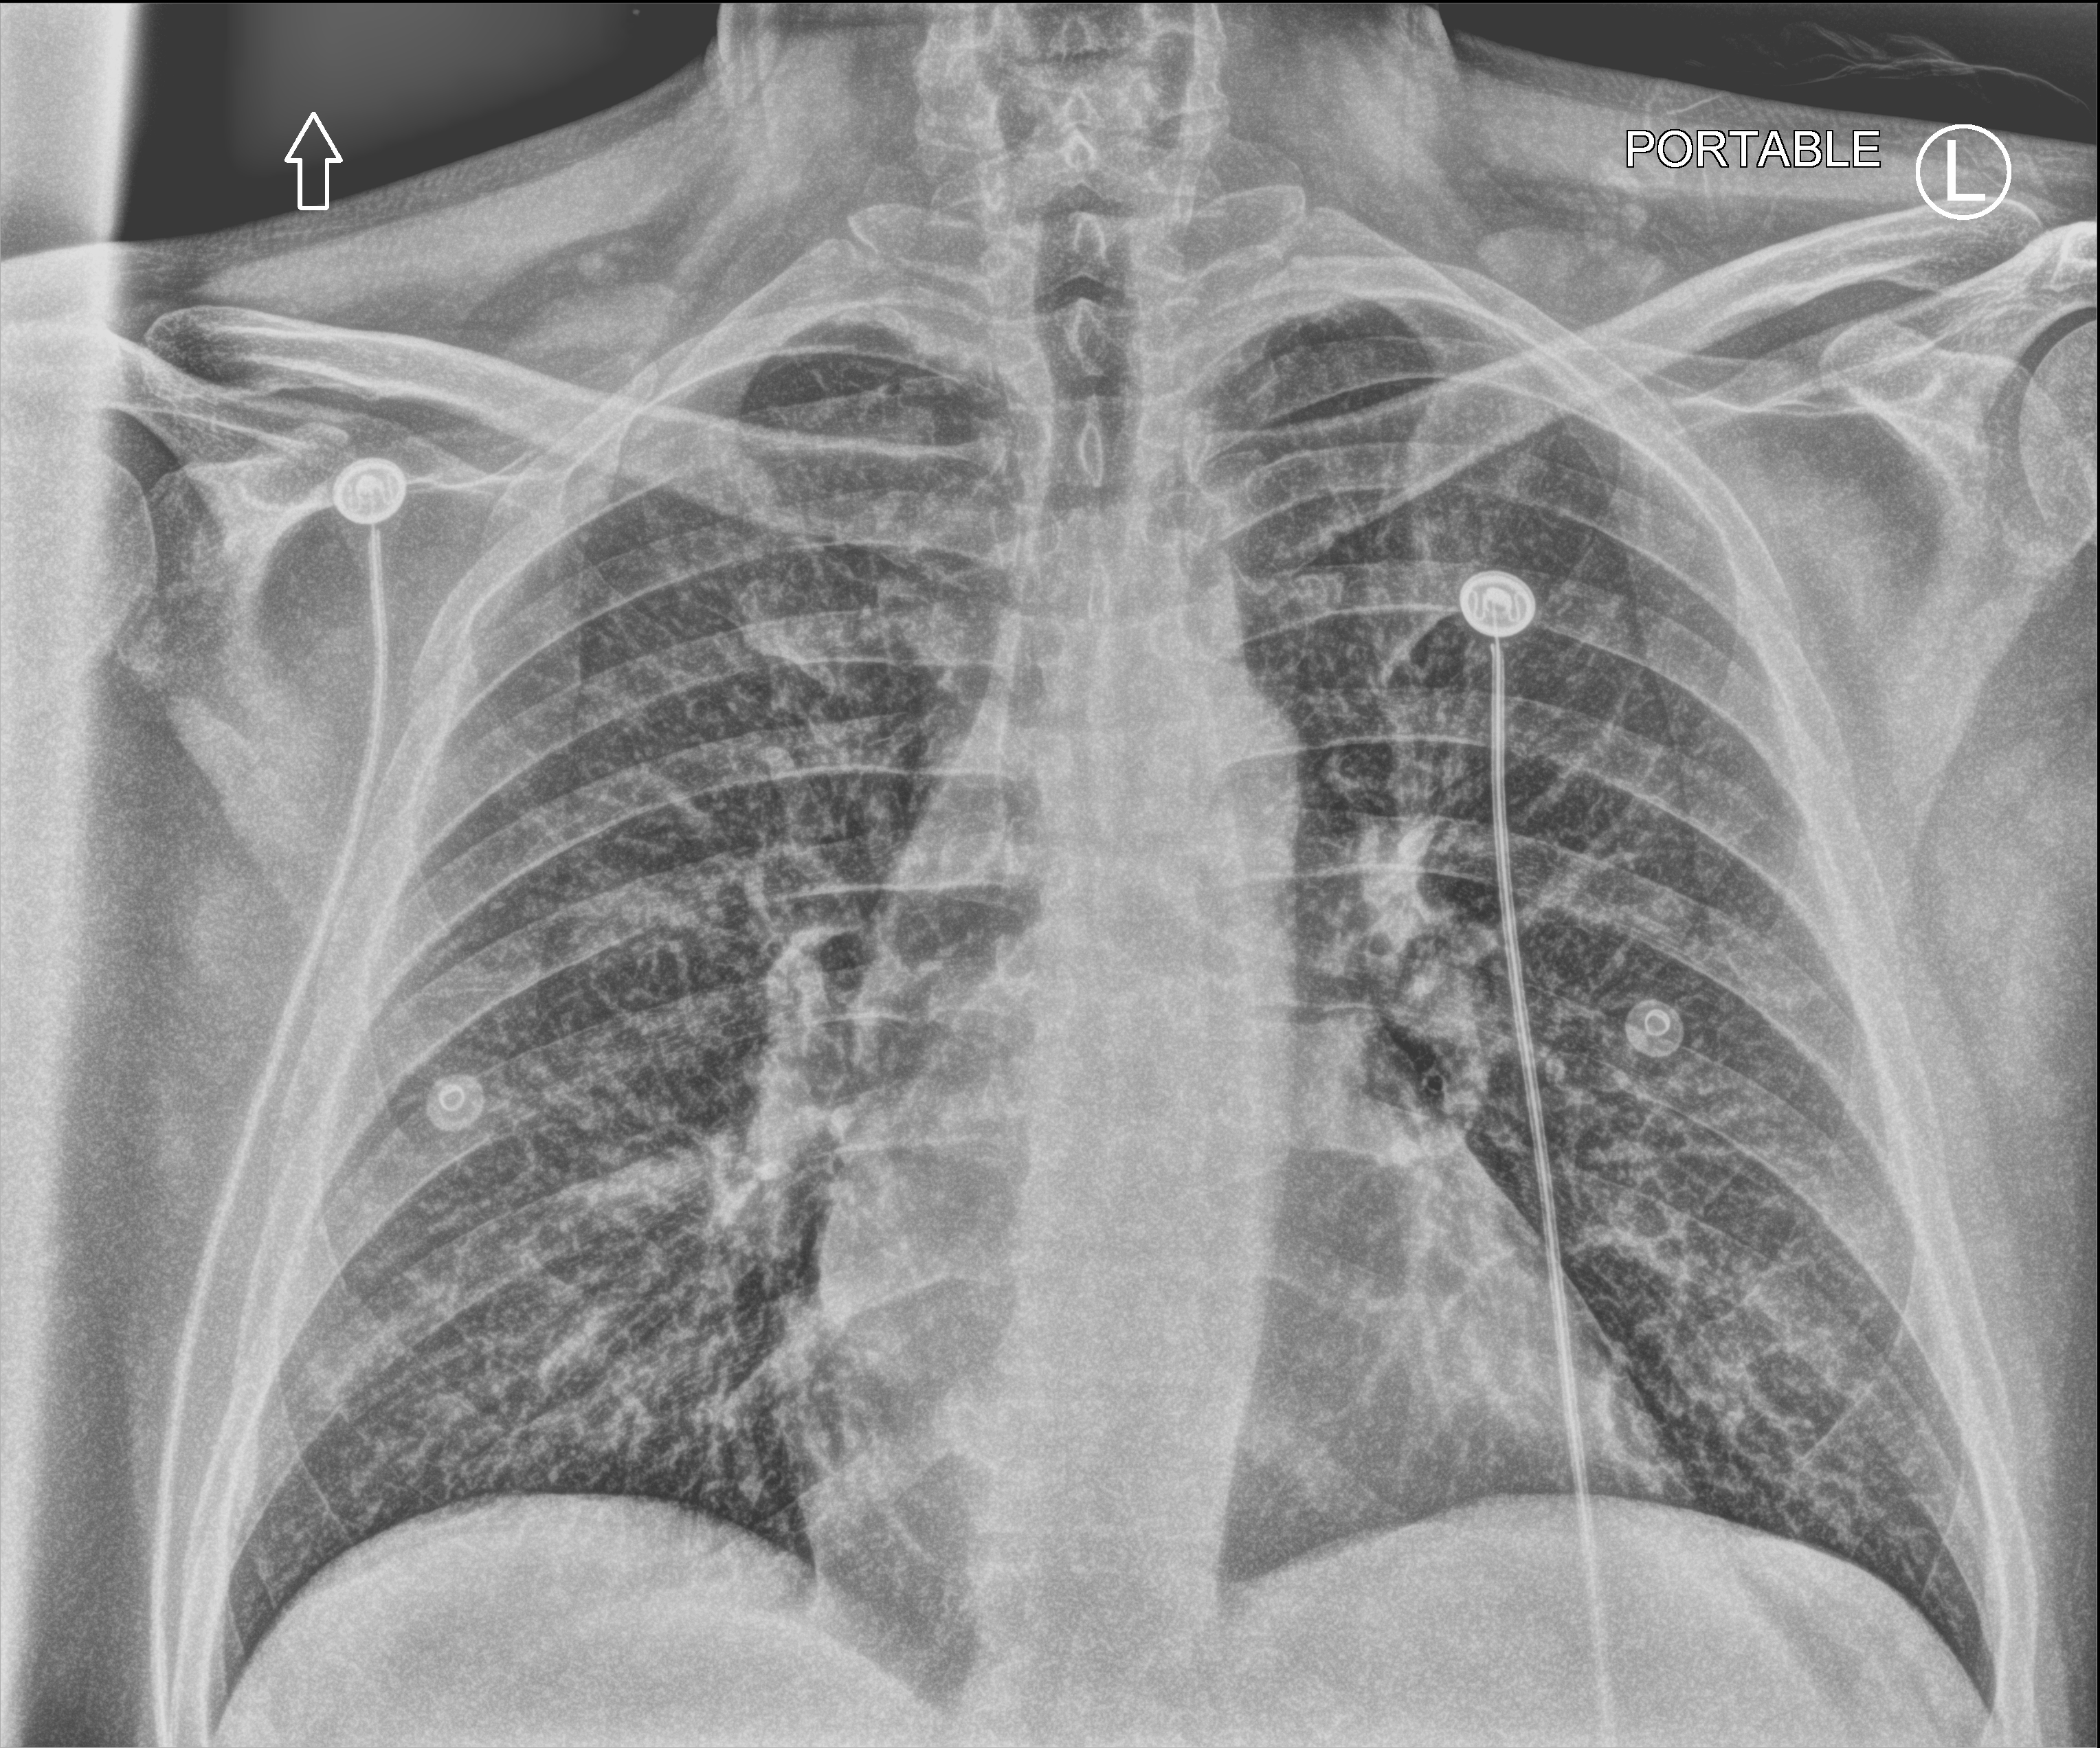
Chest X-ray (portable); anteroposterior (AP) projection. Male patient hospitalised with COVID-19, age 18–59 years.
Admission-level facts for this patient (not findings on this image; timing relative to this image not recorded): admitted to intensive care during this hospital stay: no; length of hospital stay: 3 days; mechanically ventilated during this hospital stay: no.